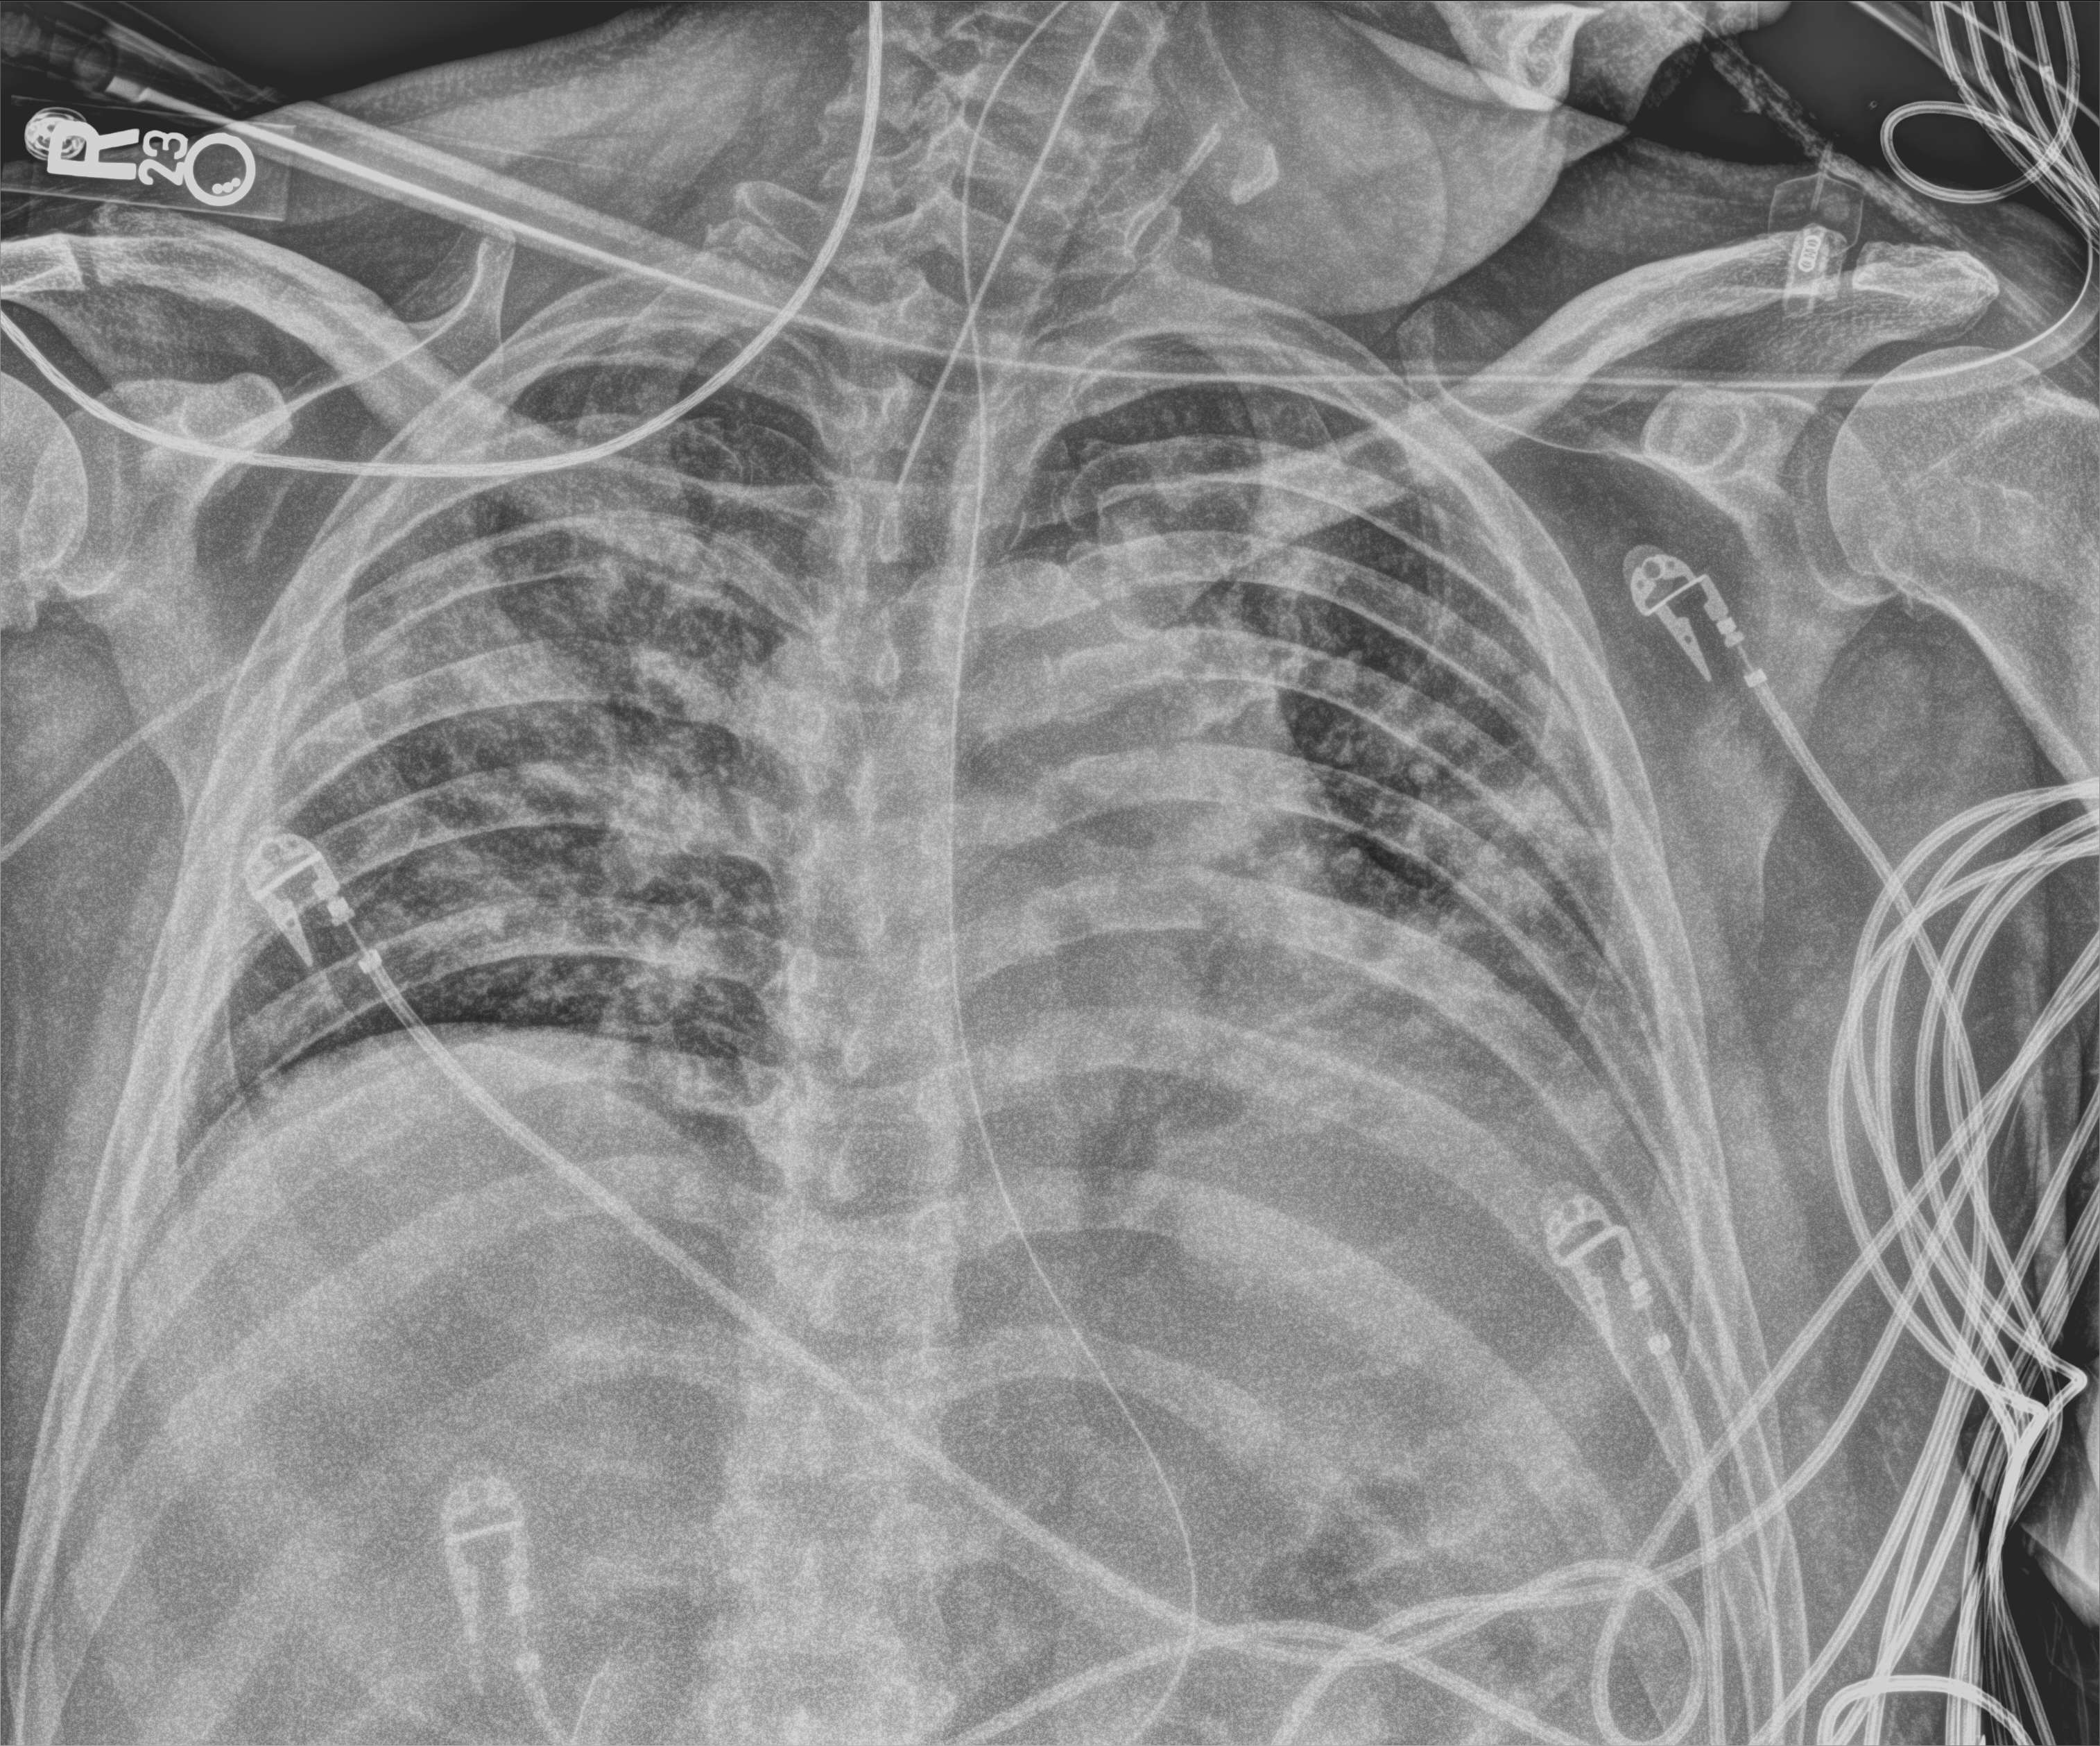
Chest X-ray (portable), anteroposterior (AP) projection. Male patient hospitalised with COVID-19, age 18–59 years.
Admission-level facts for this patient (not findings on this image; timing relative to this image not recorded): admitted to intensive care during this hospital stay: yes; mechanically ventilated during this hospital stay: yes; diabetes (admission record): yes.